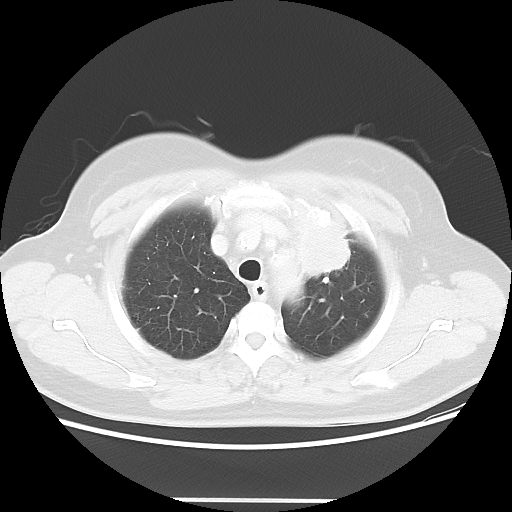
Chest CT, one axial slice. Slice 44 of 52 in the series (ordered by position). 120 kVp. Lung window (W 1500 / L -600 HU). 5 mm slice thickness. 512 × 512 image matrix, field of view 382 × 382 mm. Female patient, age 52 years. Case-level facts recorded for this patient, not image findings: clinical TNM (as recorded): T2 N3 M0.
Annotated regions visible in this slice (bounding box drawn by a radiologist):
- lung tumour (recorded histology: adenocarcinoma): bounding box <289,205,357,277> (left, top, right, bottom; pixels)